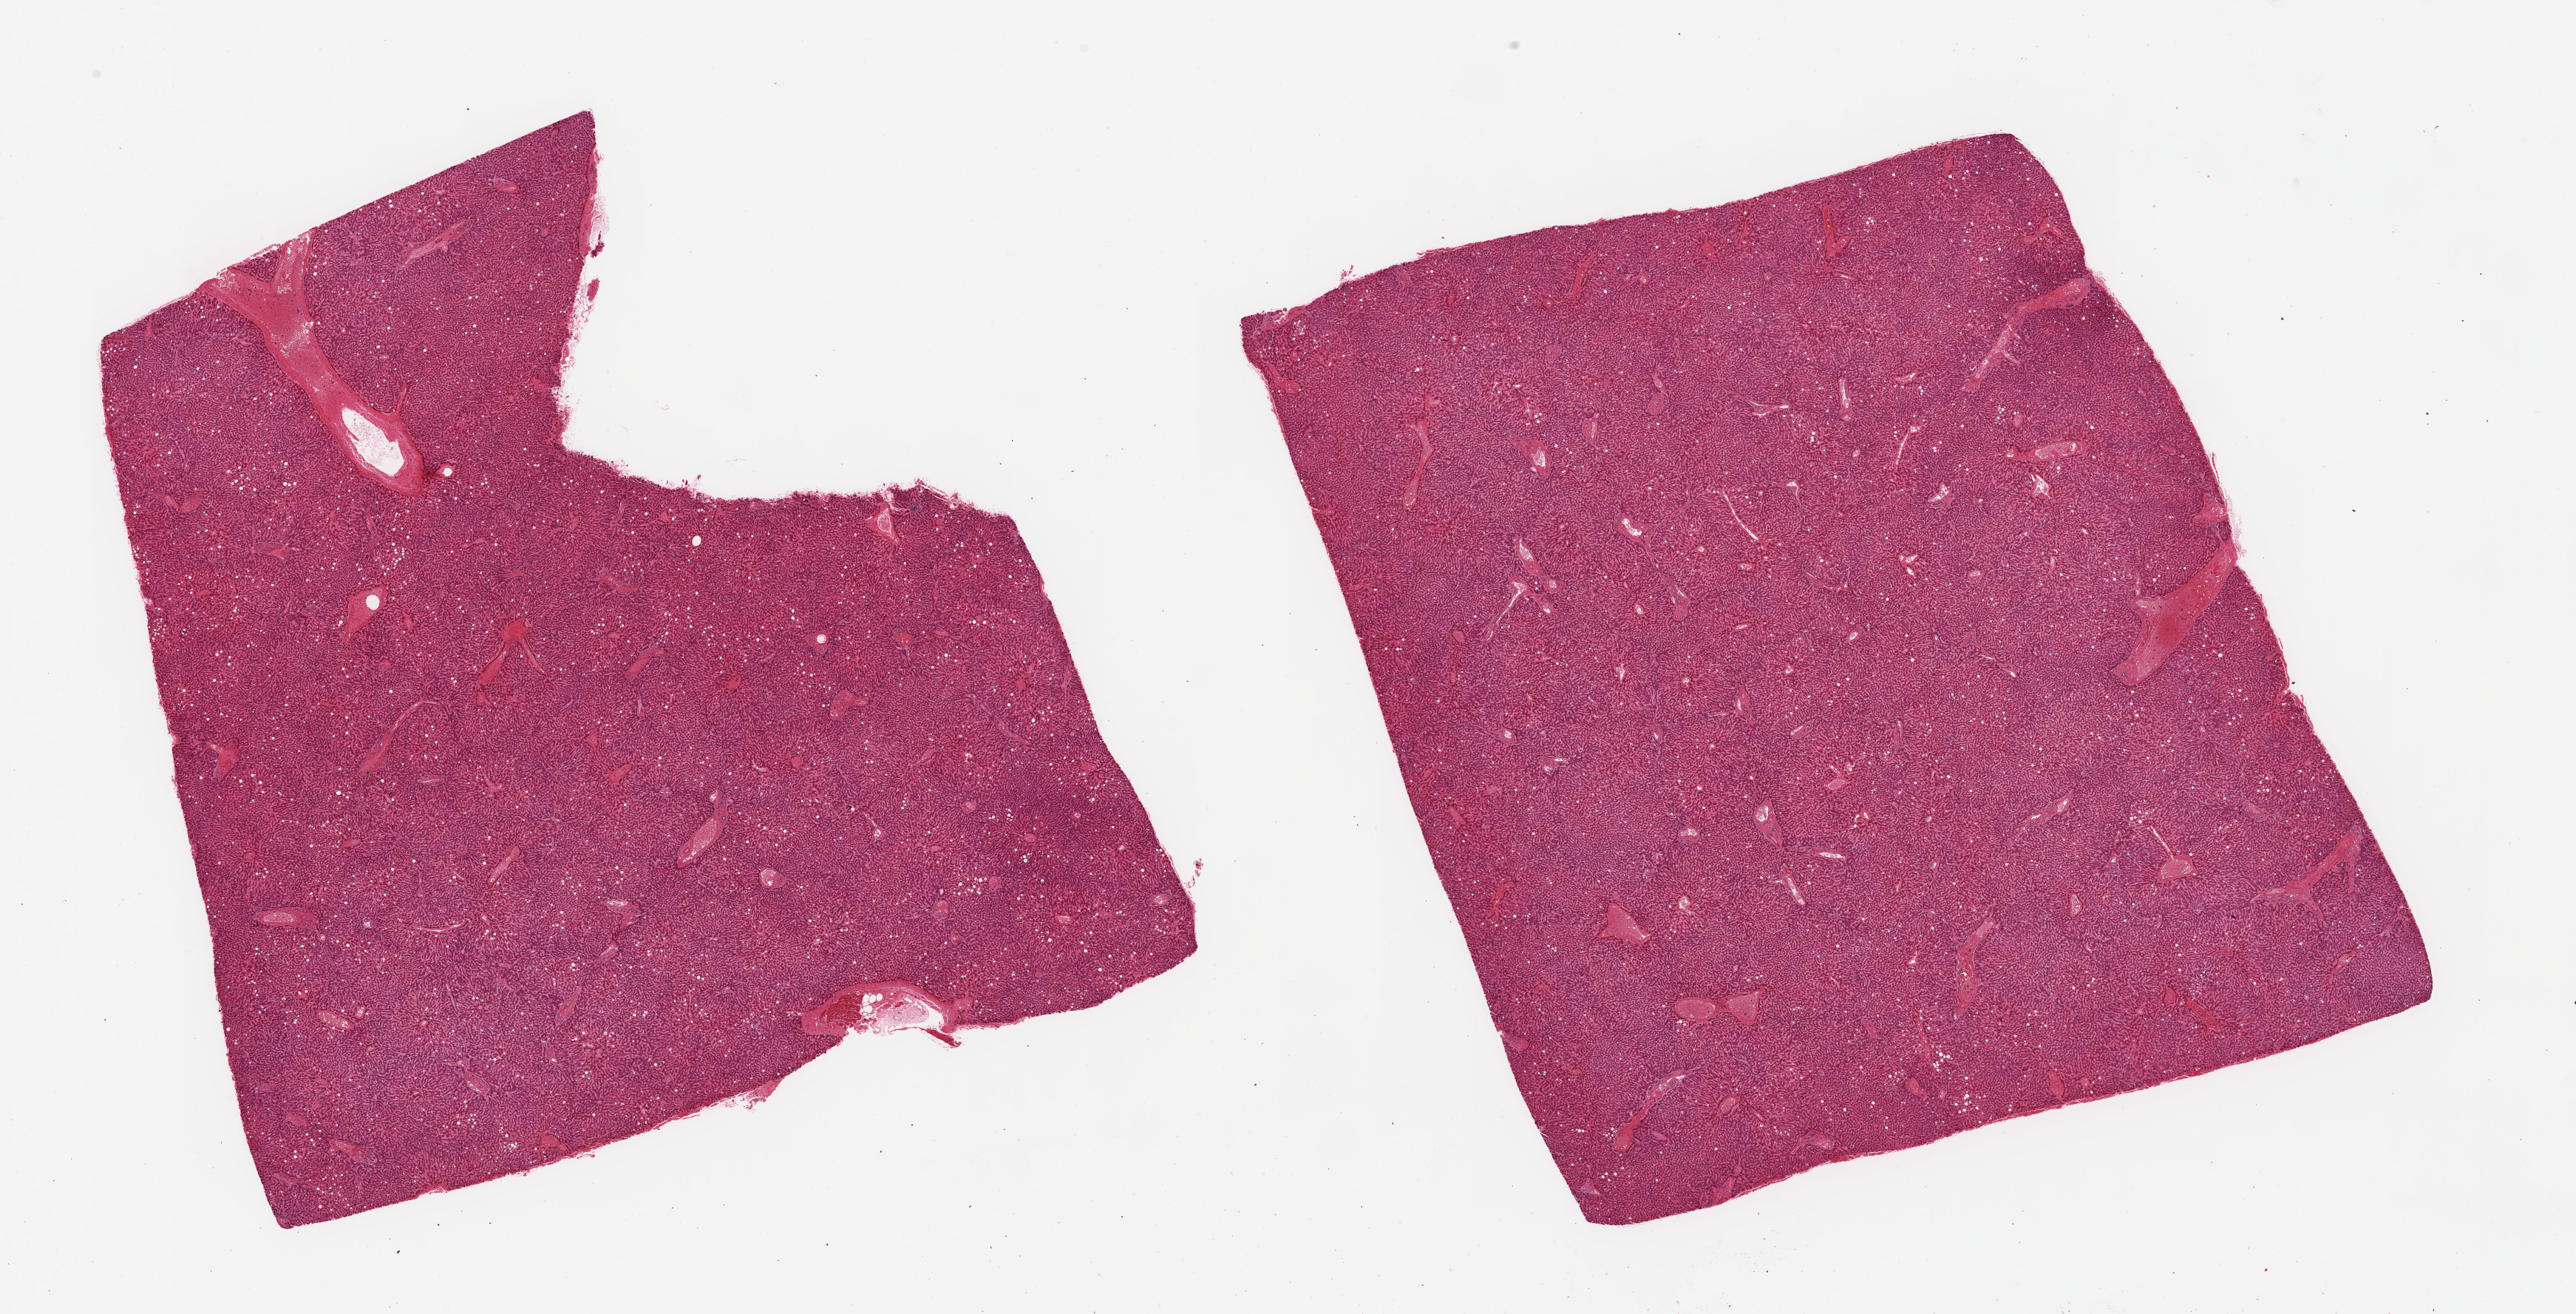
Digitized haematoxylin and eosin-stained section — shown as a low-resolution overview of the whole scanned area (about 27.6 x 14.1 mm, from a 20x scan); PAXgene-fixed, paraffin-embedded tissue; sampled site (target tissue): liver; donor tissue sample. Donor sex: male.
Reviewer comment on this tissue sample: 2 pieces, mild passive congestion.